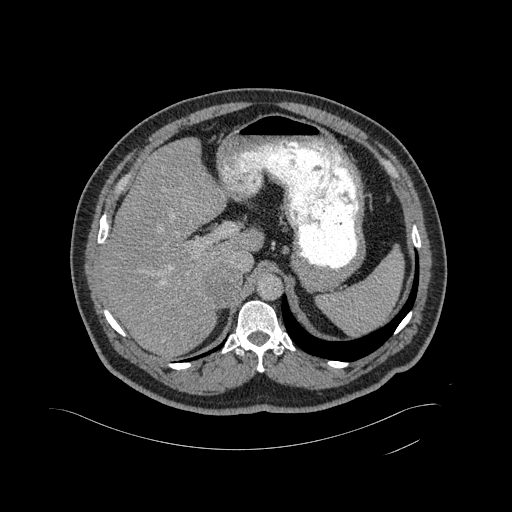
Contrast-enhanced abdominal CT, one axial slice. Position 335 of 433 along the scan axis. 120 kVp. Intravenous contrast given. Soft-tissue window (W 400 / L 40 HU). 2 mm slice thickness. 512 × 512 image matrix, field of view 500 × 500 mm. Male patient, age 56 years. Case-level facts recorded for this patient, not image findings: diagnosis: adrenocortical carcinoma; tumour side: right adrenal; tumour size at pathology: 11.6 cm; Ki-67 index: 50 %; stage (as recorded): 3.
Outlined on this slice (semi-automatic segmentation, software-assisted and operator-edited):
- mass: bounding box (x1, y1, x2, y2) in pixels: (206, 263, 241, 302)